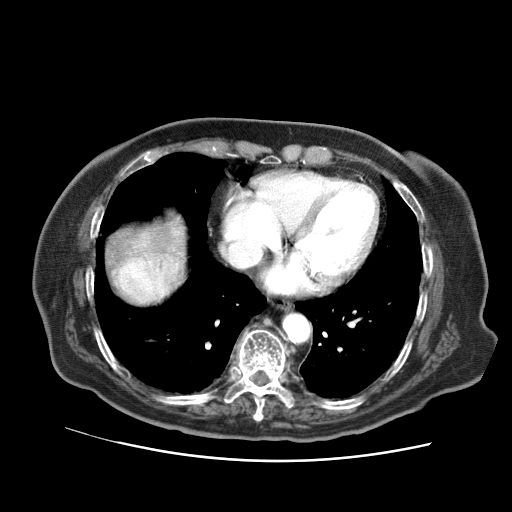
Contrast-enhanced abdominal CT (liver protocol), one axial slice; position 64 of 73 along the scan axis; reconstruction kernel STANDARD; soft-tissue window (W 400 / L 40 HU); 512 × 512 image matrix, field of view 380 × 380 mm. Case-level facts recorded for this patient, not image findings: diagnosis: hepatocellular carcinoma (patient treated with transarterial chemoembolisation; whether this scan precedes or follows treatment is not stated here); TNM stage (as recorded): Stage-I; Child-Pugh class: A; tumour differentiation: well differentiated; tumour nodularity: uninodular.
Structures marked on this image (semi-automatically segmented with operator editing):
- abdominal aorta: bounding box (x1, y1, x2, y2) in pixels: (283, 314, 310, 342)
- liver parenchyma outside the tumour (the mass and vessels are separate outlines, so this box may not span the whole liver): (104, 214, 187, 306)
- mass: (111, 254, 181, 302)